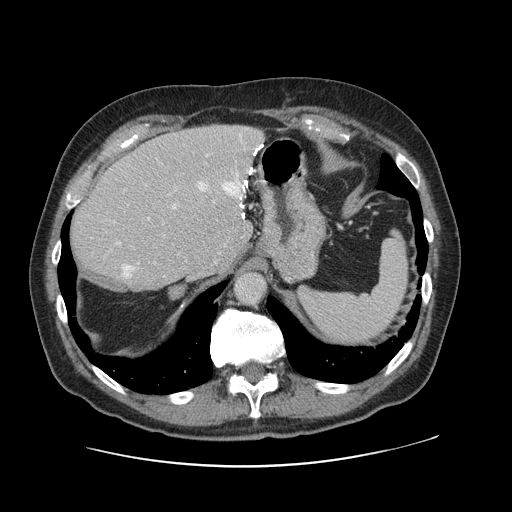
Contrast-enhanced abdominal CT, one axial slice. Slice 88 of 138 in the series (ordered by position). 120 kVp. Intravenous contrast given. Soft-tissue window (W 400 / L 40 HU). 2.5 mm slice thickness. 512 × 512 image matrix. Male patient, age 71 years. Case-level facts recorded for this patient, not image findings: diagnosis: colorectal cancer liver metastases, imaged before liver resection; multiple liver metastases: no; largest metastasis: 3.3 cm; disease in both lobes: no.
Outlined on this slice (expert manual segmentation):
- hepatic veins: box from (x=122, y=146) to (x=261, y=278) px
- liver: (x=70, y=125)–(x=263, y=292)
- planned liver remnant (the part of the liver to remain after resection): (x=70, y=153)–(x=241, y=292)
- portal vein (with intrahepatic branches): (x=115, y=203)–(x=178, y=245)